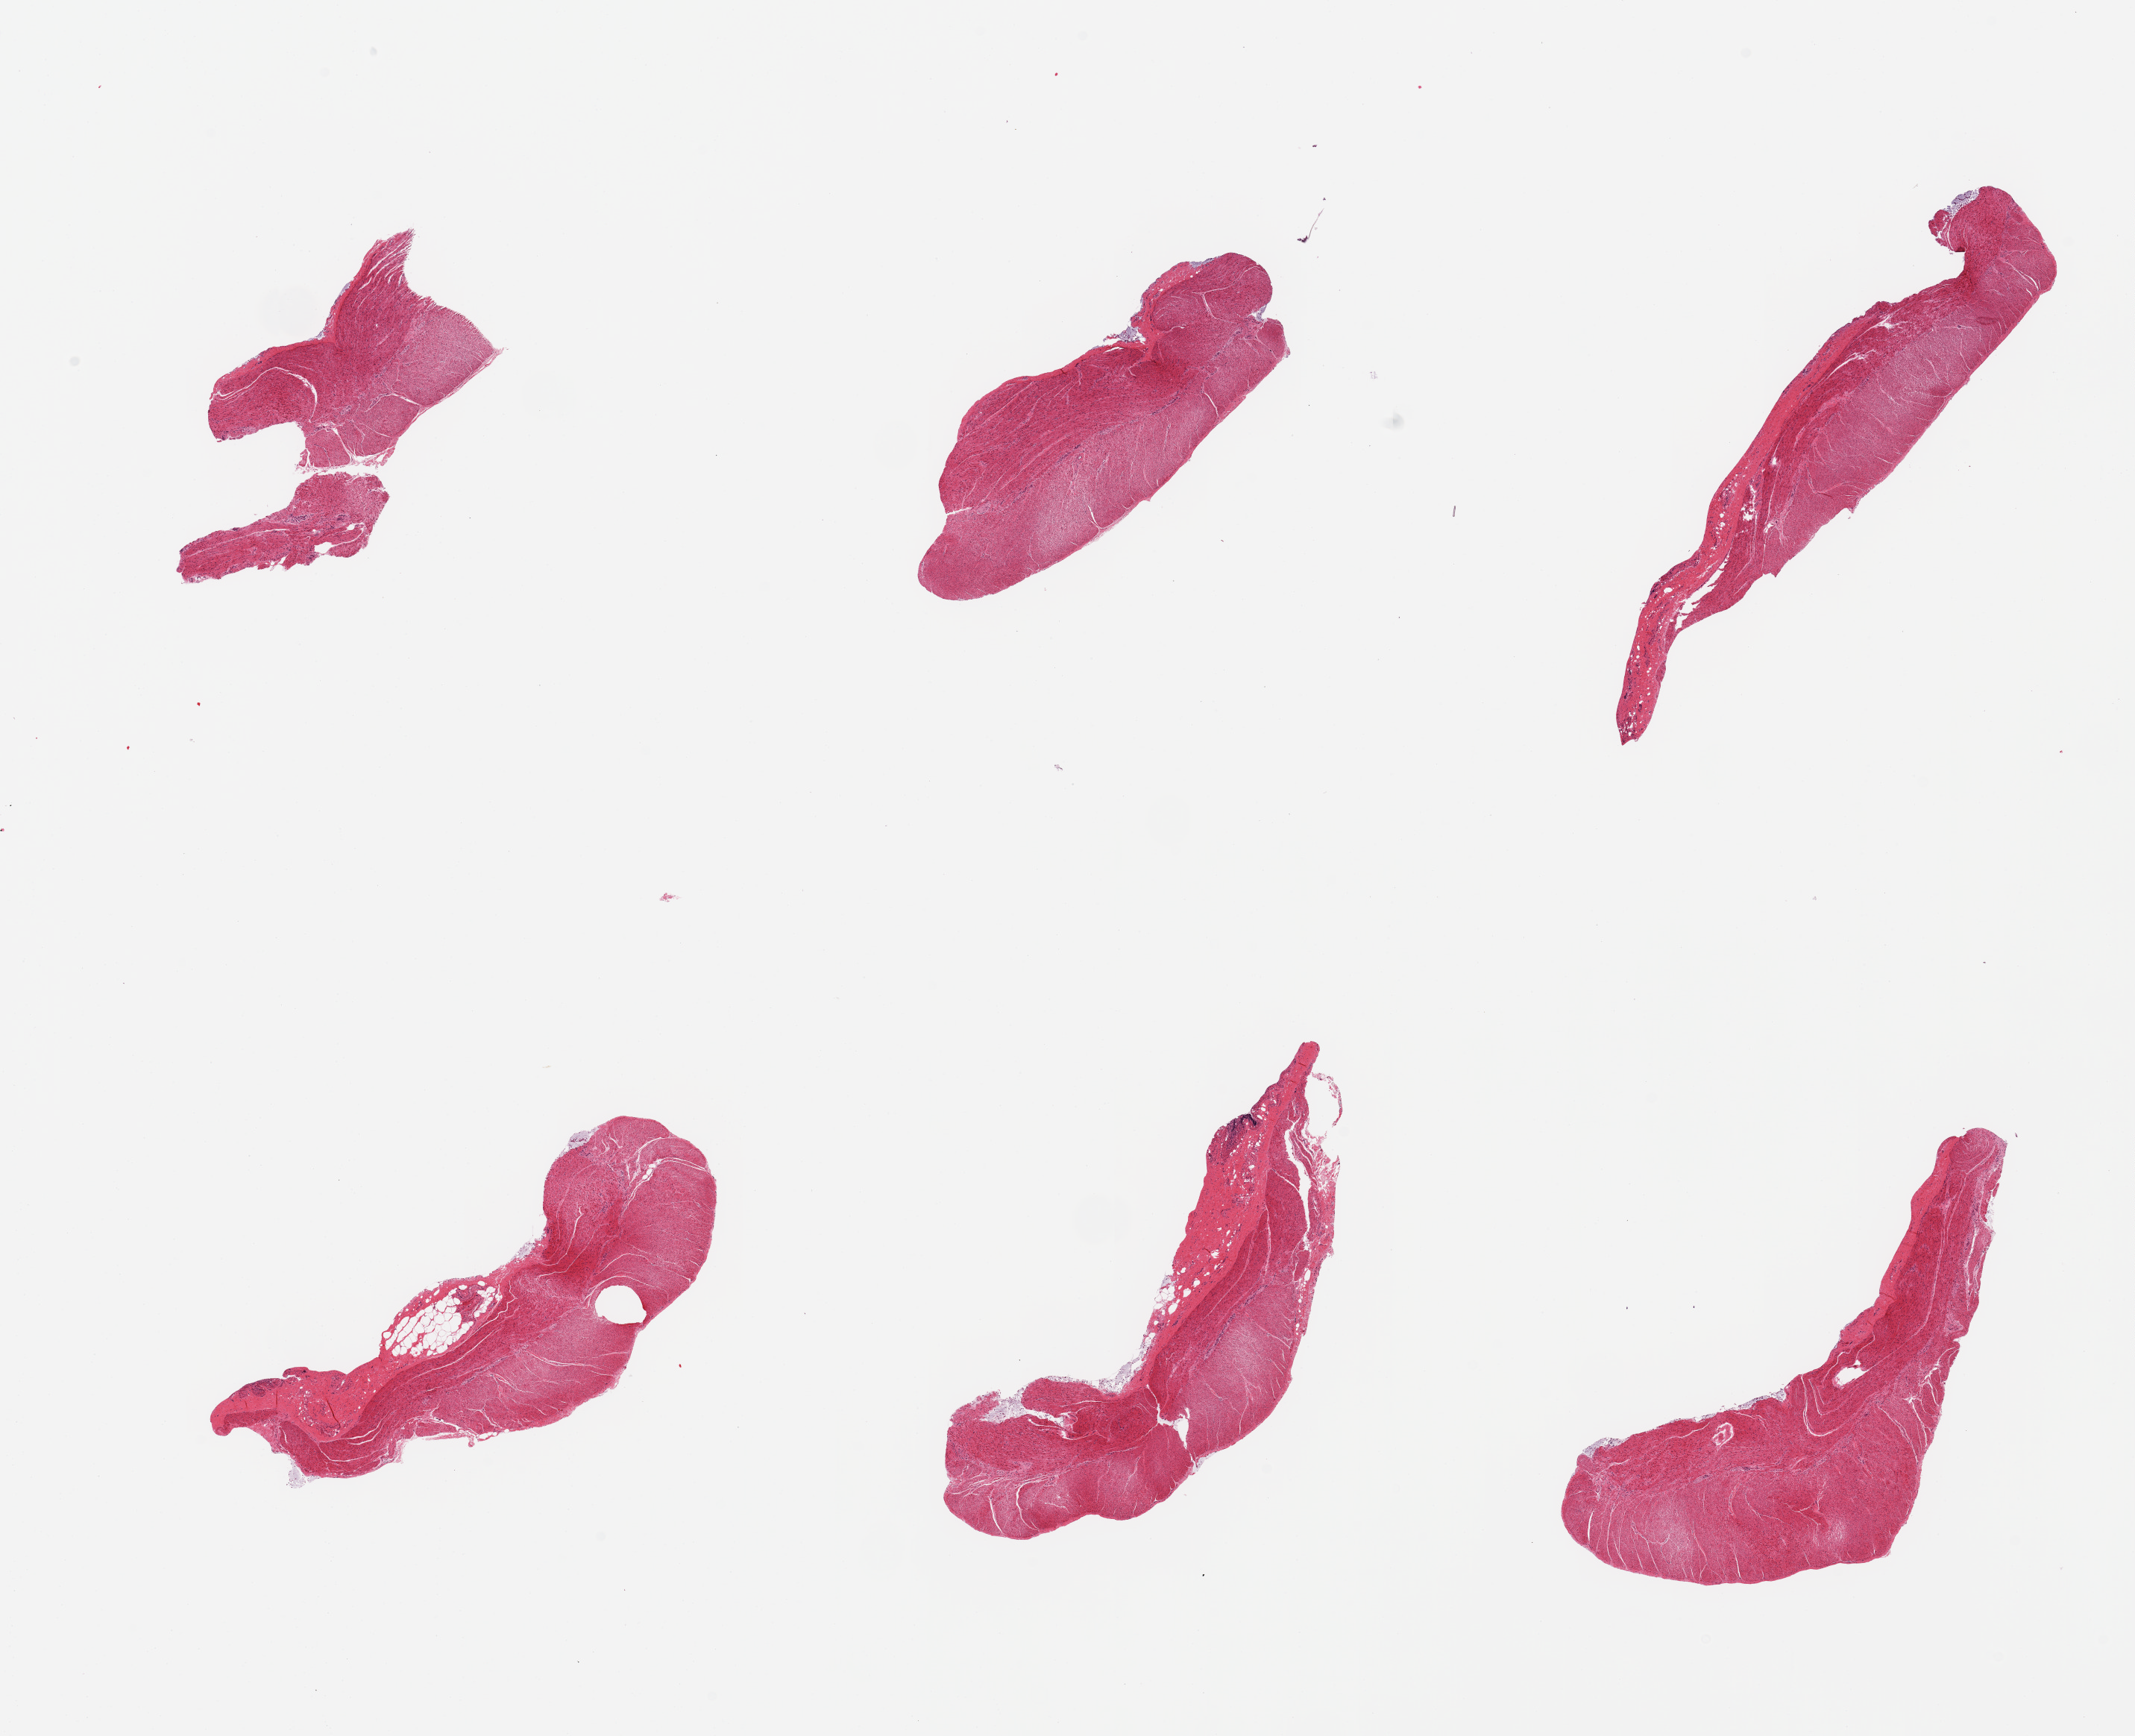
Digitized H&E-stained section — low-resolution overview of the scanned area, about 22.6 x 18.4 mm, PAXgene-fixed, paraffin-embedded tissue, target tissue: sigmoid colon, tissue donor sample. Male donor.
Review note (as recorded): 6 pieces; minimal residual attached autolyzed mocosa.